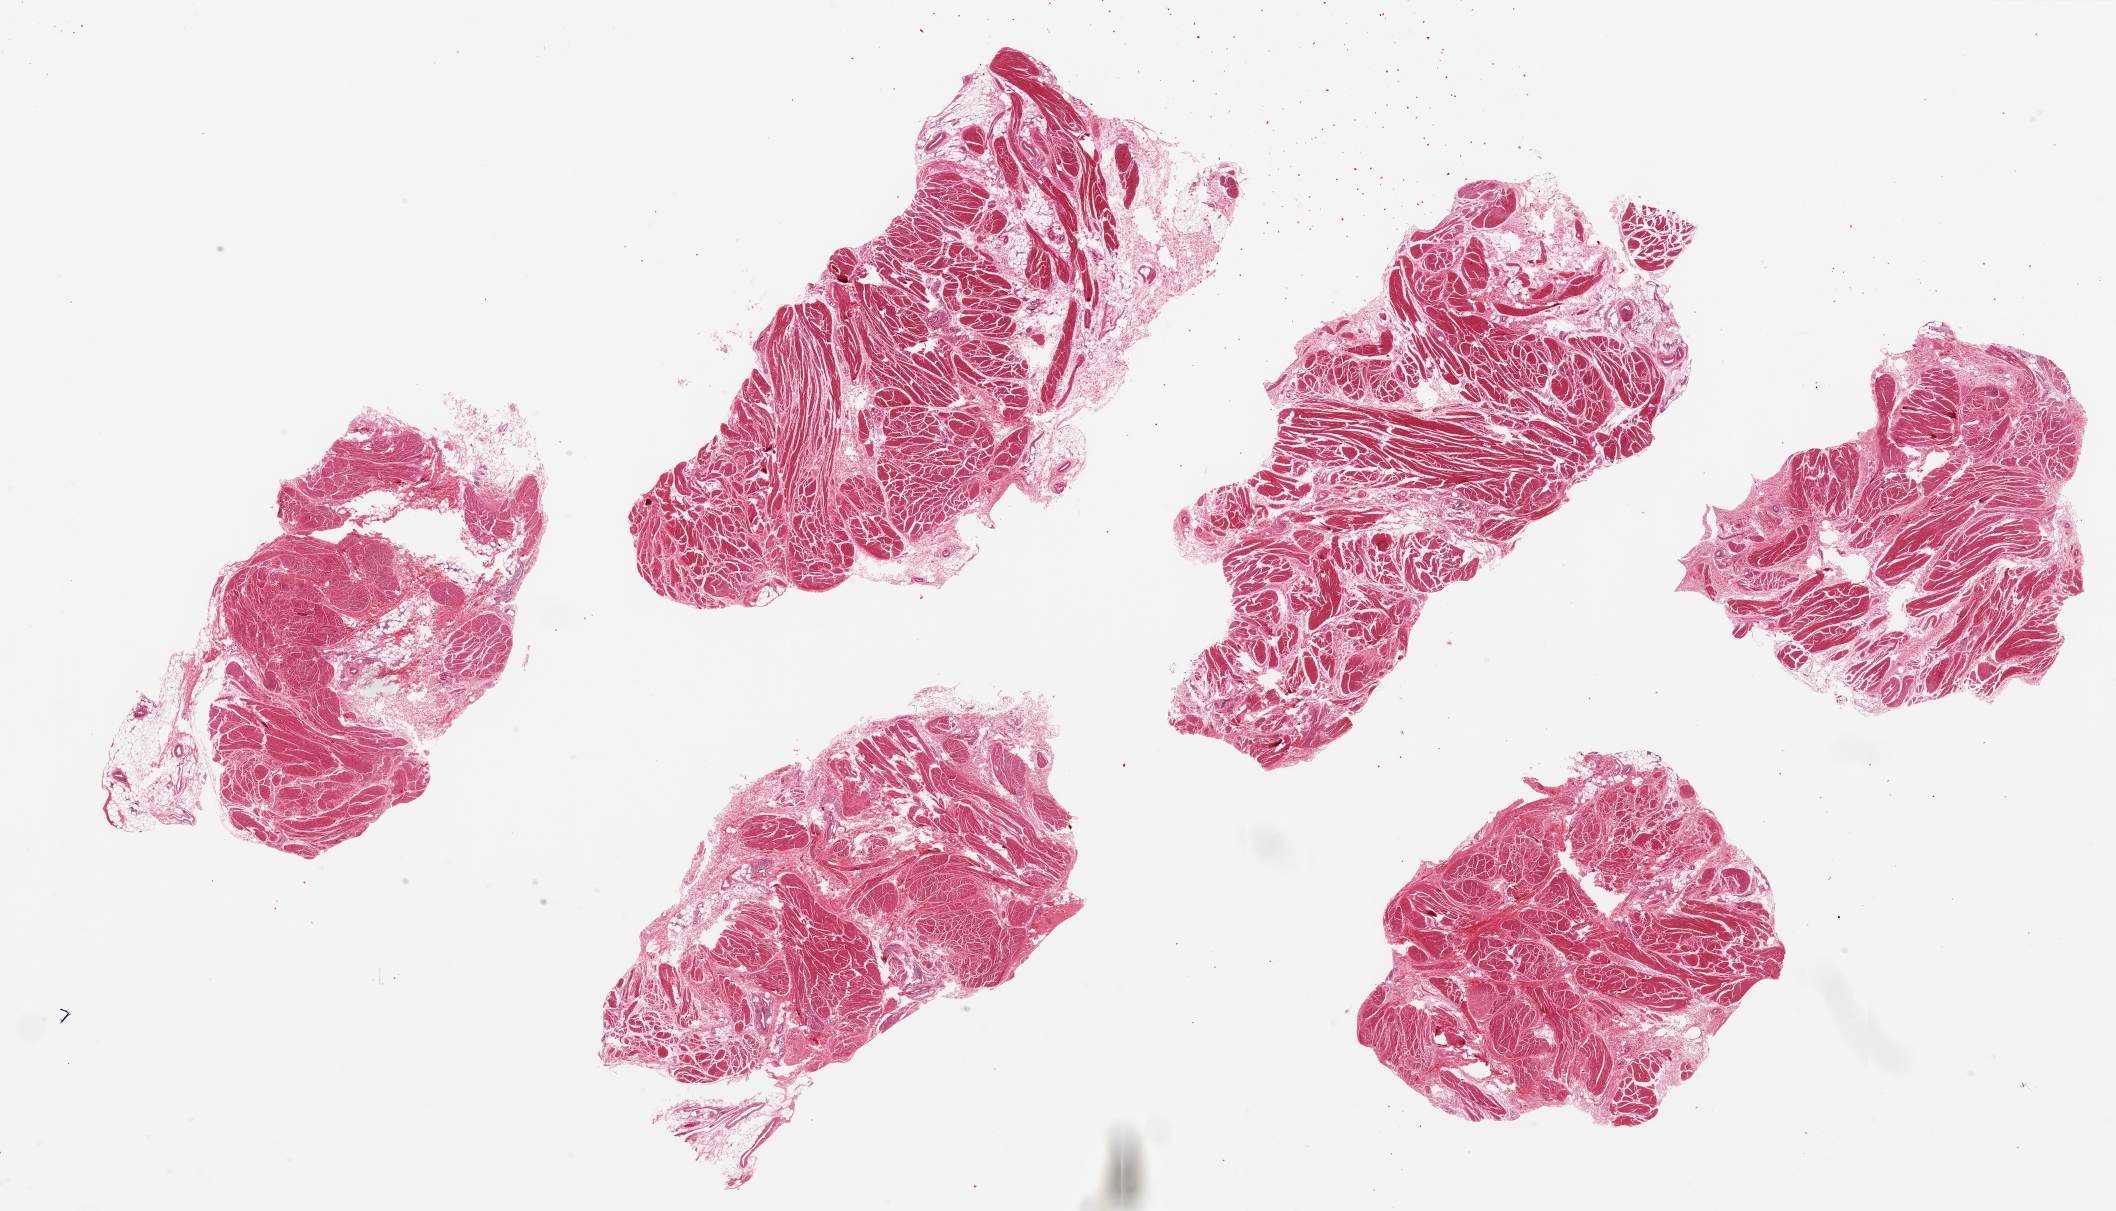
Digitized hematoxylin and eosin (H&E)-stained section, a low-resolution overview of the entire scanned area, about 33.5 x 19.2 mm. PAXgene-fixed paraffin-embedded (PFPE) section. Sampled site (target tissue): urinary bladder. Donor tissue sample. Donor sex: male.
- review note (as recorded): 6 pieces up to 10x5 mm; mucosa not in sections